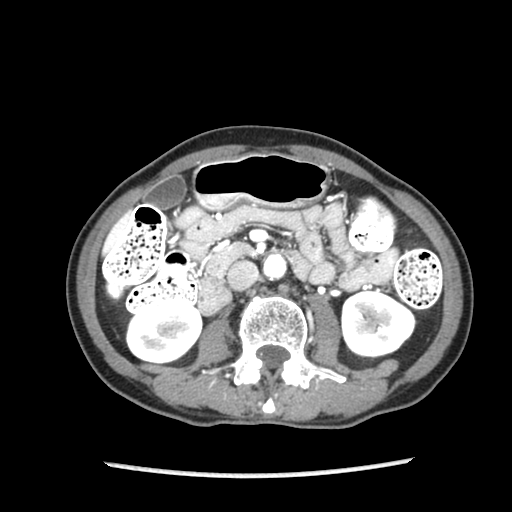
Contrast-enhanced abdominal CT (liver protocol), one axial slice. Reconstruction kernel STANDARD. Soft-tissue window (W 400 / L 40 HU). 2.5 mm slice thickness. 512 × 512 image matrix, field of view 300 × 300 mm. From the clinical record (not read from this slice): diagnosis: hepatocellular carcinoma (patient treated with transarterial chemoembolisation; whether this scan precedes or follows treatment is not stated here); TNM stage (as recorded): Stage-IIIB; Child-Pugh class: A; tumour differentiation: well differentiated.
Structures marked on this image (semi-automatically segmented with operator editing):
- liver parenchyma outside the tumour (the mass and vessels are separate outlines, so this box may not span the whole liver): box from (x=117, y=215) to (x=128, y=225) px